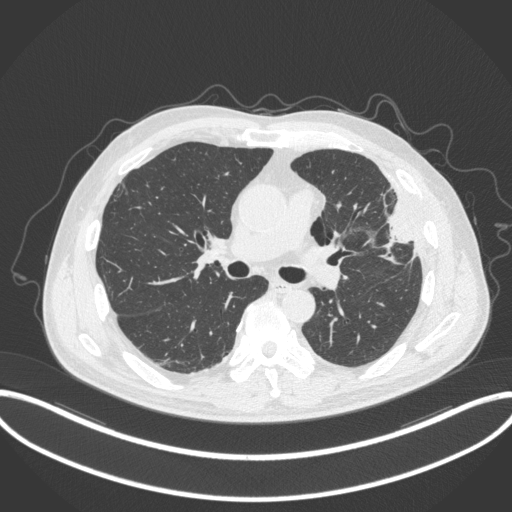
Chest CT, one axial slice; lung window (W 1500 / L -600 HU); 1 mm slice thickness; 512 × 512 image matrix, field of view 415 × 415 mm. Male patient, age 64 years. From the clinical record (not read from this slice): clinical TNM (as recorded): T4 N1 M0.
Structures marked on this image (bounding box drawn by a radiologist):
- lung tumour (recorded histology: adenocarcinoma): bounding box (x1, y1, x2, y2) in pixels: (382, 193, 420, 257)